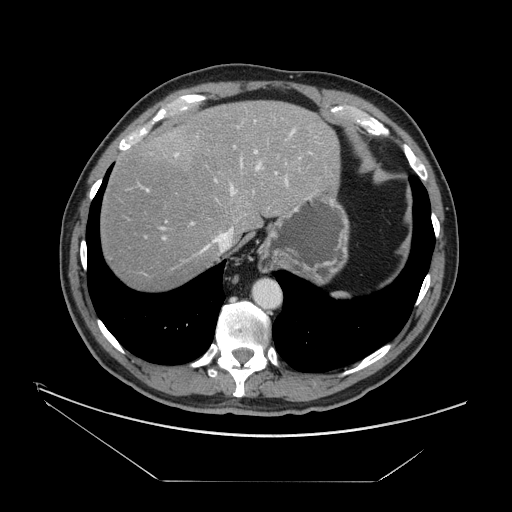
Contrast-enhanced abdominal CT, one axial slice. Position 128 of 161 along the scan axis. Reconstruction kernel STANDARD. 120 kVp. Intravenous contrast given. Soft-tissue window (W 400 / L 40 HU). 2.5 mm slice thickness. 512 × 512 image matrix. Male patient, age 65 years. From the clinical record (not read from this slice): diagnosis: colorectal cancer liver metastases, imaged before liver resection; multiple liver metastases: yes; largest metastasis: 4.2 cm; disease in both lobes: yes.
Annotated regions visible in this slice (manually delineated by an expert):
- hepatic veins: bounding box [x1, y1, x2, y2] px = [198, 126, 295, 255]
- liver: [100, 101, 338, 290]
- planned liver remnant (the part of the liver to remain after resection): [100, 101, 338, 290]
- portal vein (with intrahepatic branches): [141, 118, 312, 240]